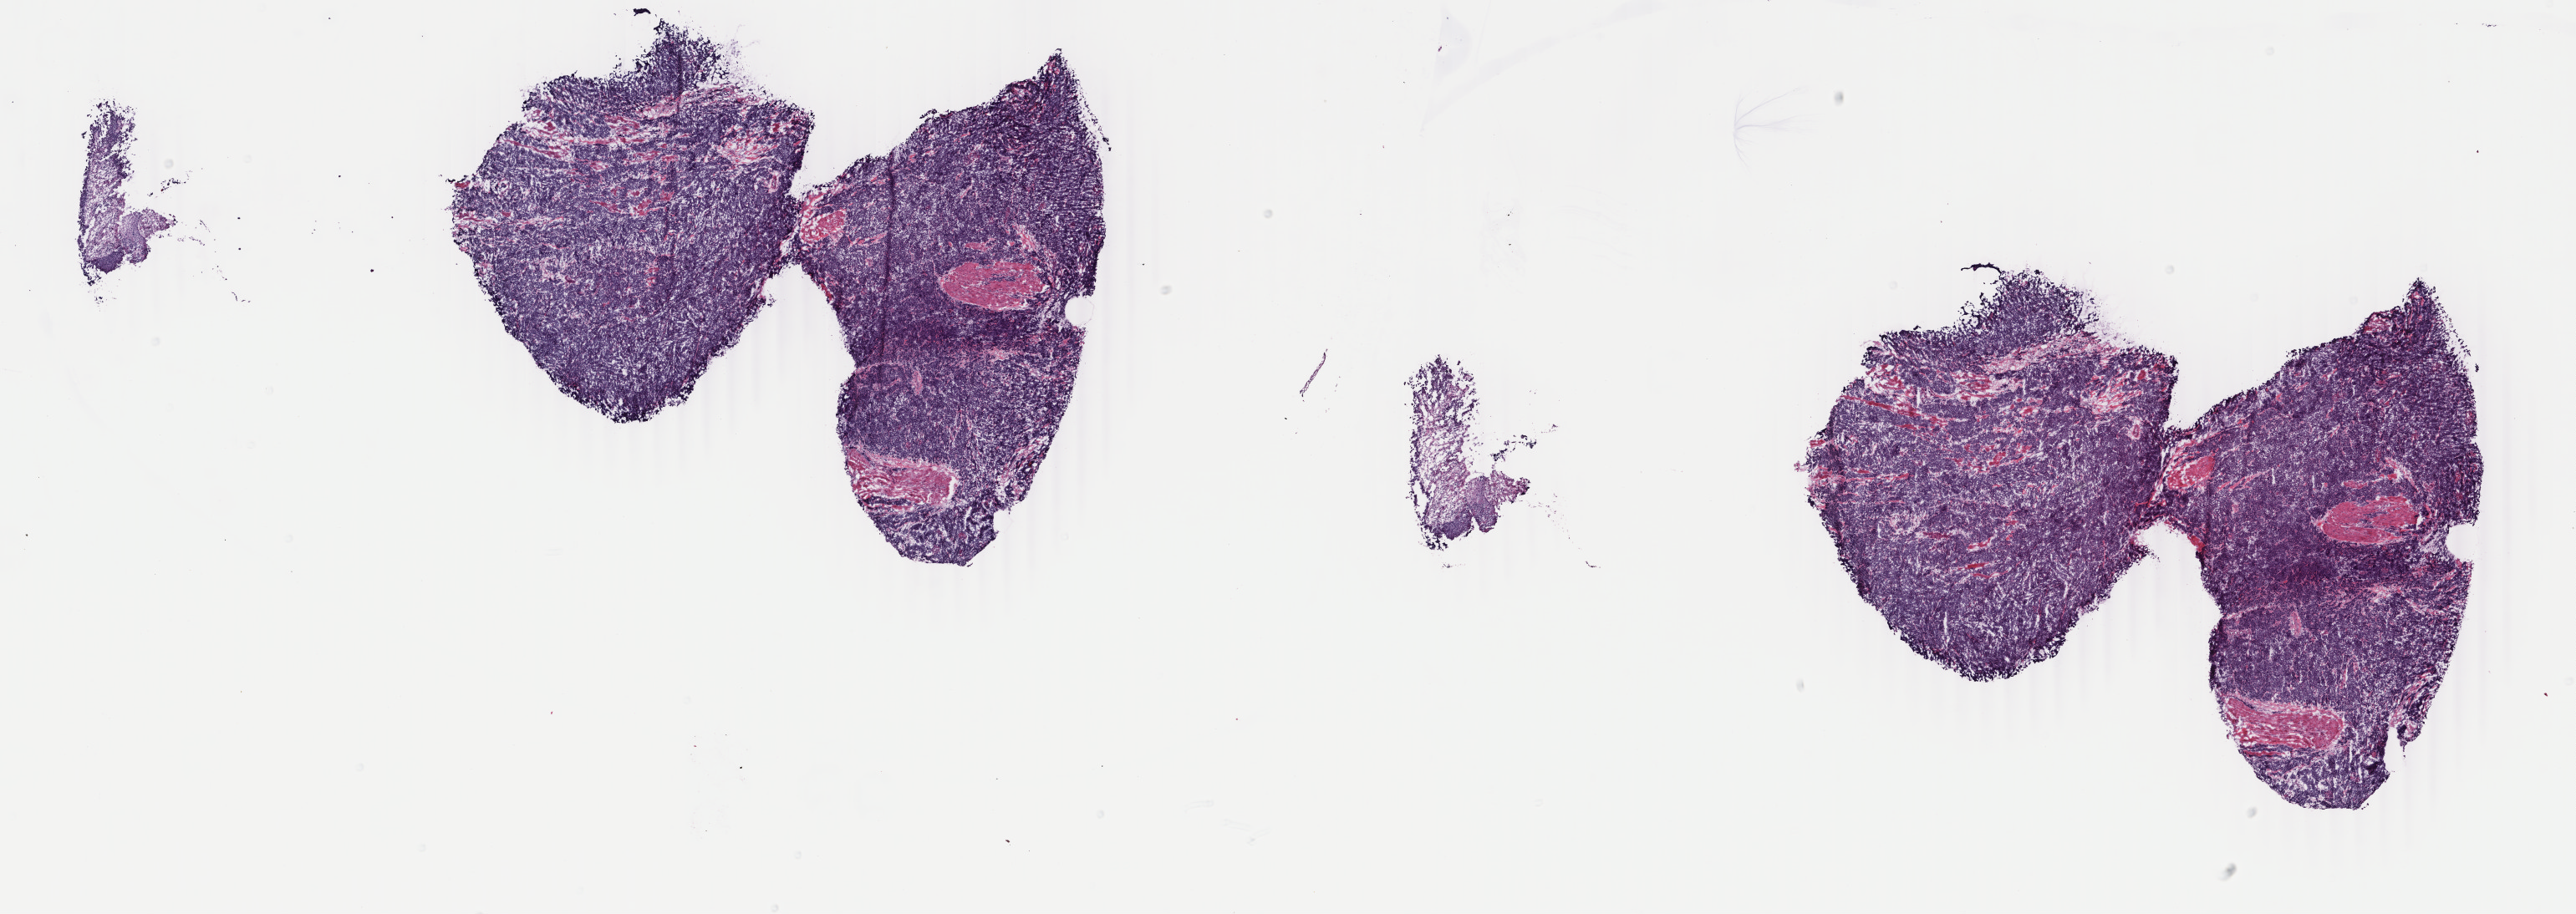
H&E-stained whole-slide image, shown as a low-resolution overview of the whole scanned area (about 24.5 x 8.7 mm). Frozen section. Sample: primary tumour, bladder. Female patient; age at initial diagnosis 68 years. Histologic grade: high grade. Pathologist review of this section (percent, as recorded): tumour cells 89%, tumour nuclei 97%, normal cells 5%, stromal cells 1%, necrosis 5%. Infiltration values recorded for this section: lymphocyte infiltration 0%, monocyte infiltration 0%, neutrophil infiltration 0%.
• histologic diagnosis: Transitional cell carcinoma
• TNM: T3a N1 M1
• AJCC pathologic stage: IV